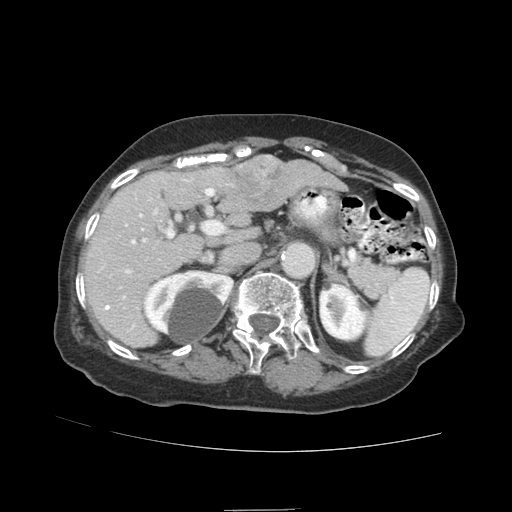
Contrast-enhanced abdominal CT (liver protocol), one axial slice. Slice 54 of 89 in the series (ordered by position). Reconstruction kernel STANDARD. Soft-tissue window (W 400 / L 40 HU). 2.5 mm slice thickness. 512 × 512 image matrix. Case-level facts recorded for this patient, not image findings: diagnosis: hepatocellular carcinoma (patient treated with transarterial chemoembolisation; whether this scan precedes or follows treatment is not stated here); TNM stage (as recorded): Stage-II; Child-Pugh class: A; tumour size: 4 cm.
Annotated regions visible in this slice (semi-automatic segmentation, software-assisted and operator-edited):
- liver parenchyma outside the tumour (the mass and vessels are separate outlines, so this box may not span the whole liver): bounding box <84,156,332,346> (left, top, right, bottom; pixels)
- mass: <232,155,291,212>
- liver vessels: <90,178,232,332>